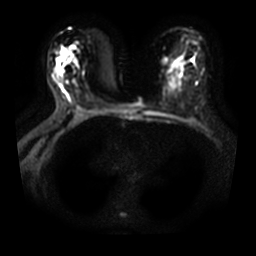
Breast MRI, one axial slice. Slice 20 of 33 in the series (ordered by position). Diffusion-weighted series; image 2 of 4 stored at this slice position (different b-values; order by instance number). 3 T. 256 × 256 image matrix, field of view 350 × 350 mm. Female patient.
Annotated regions visible in this slice (manually delineated by an expert):
- tumour on diffusion-weighted imaging: bounding box (x1, y1, x2, y2) in pixels: (60, 49, 66, 60)